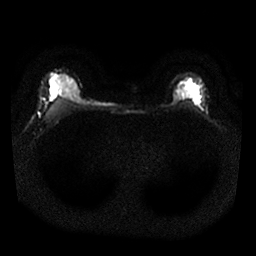
Breast MRI, one axial slice; slice 22 of 25 in the series (ordered by position); diffusion-weighted series; image 2 of 4 stored at this slice position (different b-values; order by instance number); 1.5 T; 4 mm slice thickness; 256 × 256 image matrix. Female patient.
Annotated regions visible in this slice (outlined manually by an expert reader):
- tumour on diffusion-weighted imaging: bounding box <177,88,179,91> (left, top, right, bottom; pixels)